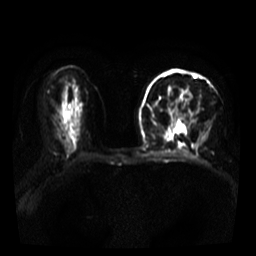
Breast MRI, one axial slice; slice 21 of 39 in the series (ordered by position); diffusion-weighted series; image 2 of 4 stored at this slice position (different b-values; order by instance number); 3 T; 5 mm slice thickness; 256 × 256 image matrix, field of view 320 × 320 mm. Female patient.
Annotated regions visible in this slice (manually delineated by an expert):
- tumour on diffusion-weighted imaging: bounding box [x1, y1, x2, y2] px = [187, 92, 192, 99]